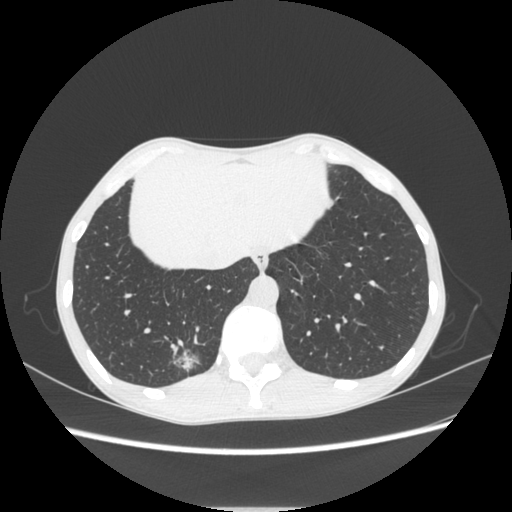
Chest CT, one axial slice. Slice 63 of 272 in the series (ordered by position). Reconstruction kernel STANDARD. 120 kVp. Lung window (W 1500 / L -600 HU). 512 × 512 image matrix, field of view 350 × 350 mm. Patient: female, 51 years. Case-level facts recorded for this patient, not image findings: clinical TNM (as recorded): T1c N0 M0; histopathological grade: G2-3.
Annotated regions visible in this slice (bounding box drawn by a radiologist):
- lung tumour (recorded histology: adenocarcinoma): bounding box <170,339,207,383> (left, top, right, bottom; pixels)